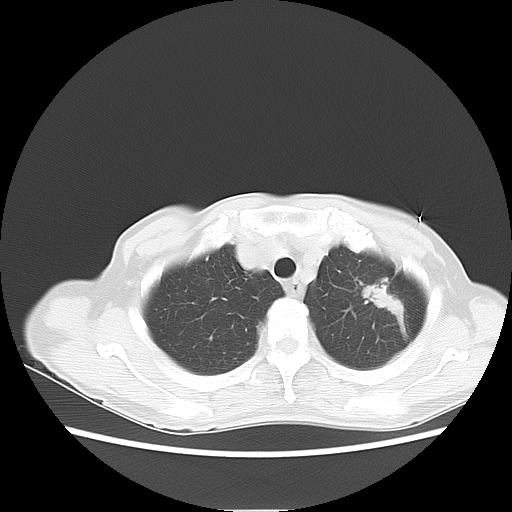
Chest CT, one axial slice. Slice 11 of 14 in the series (ordered by position). Reconstruction kernel LUNG. 120 kVp. Lung window (W 1500 / L -600 HU). 5 mm slice thickness. 512 × 512 image matrix. Female patient, age 71 years. Case-level facts recorded for this patient, not image findings: clinical TNM (as recorded): T2 N0 M0.
Annotated regions visible in this slice (rectangle marked by the reading radiologist):
- lung tumour (recorded histology: adenocarcinoma): bounding box (x1, y1, x2, y2) in pixels: (357, 277, 406, 320)